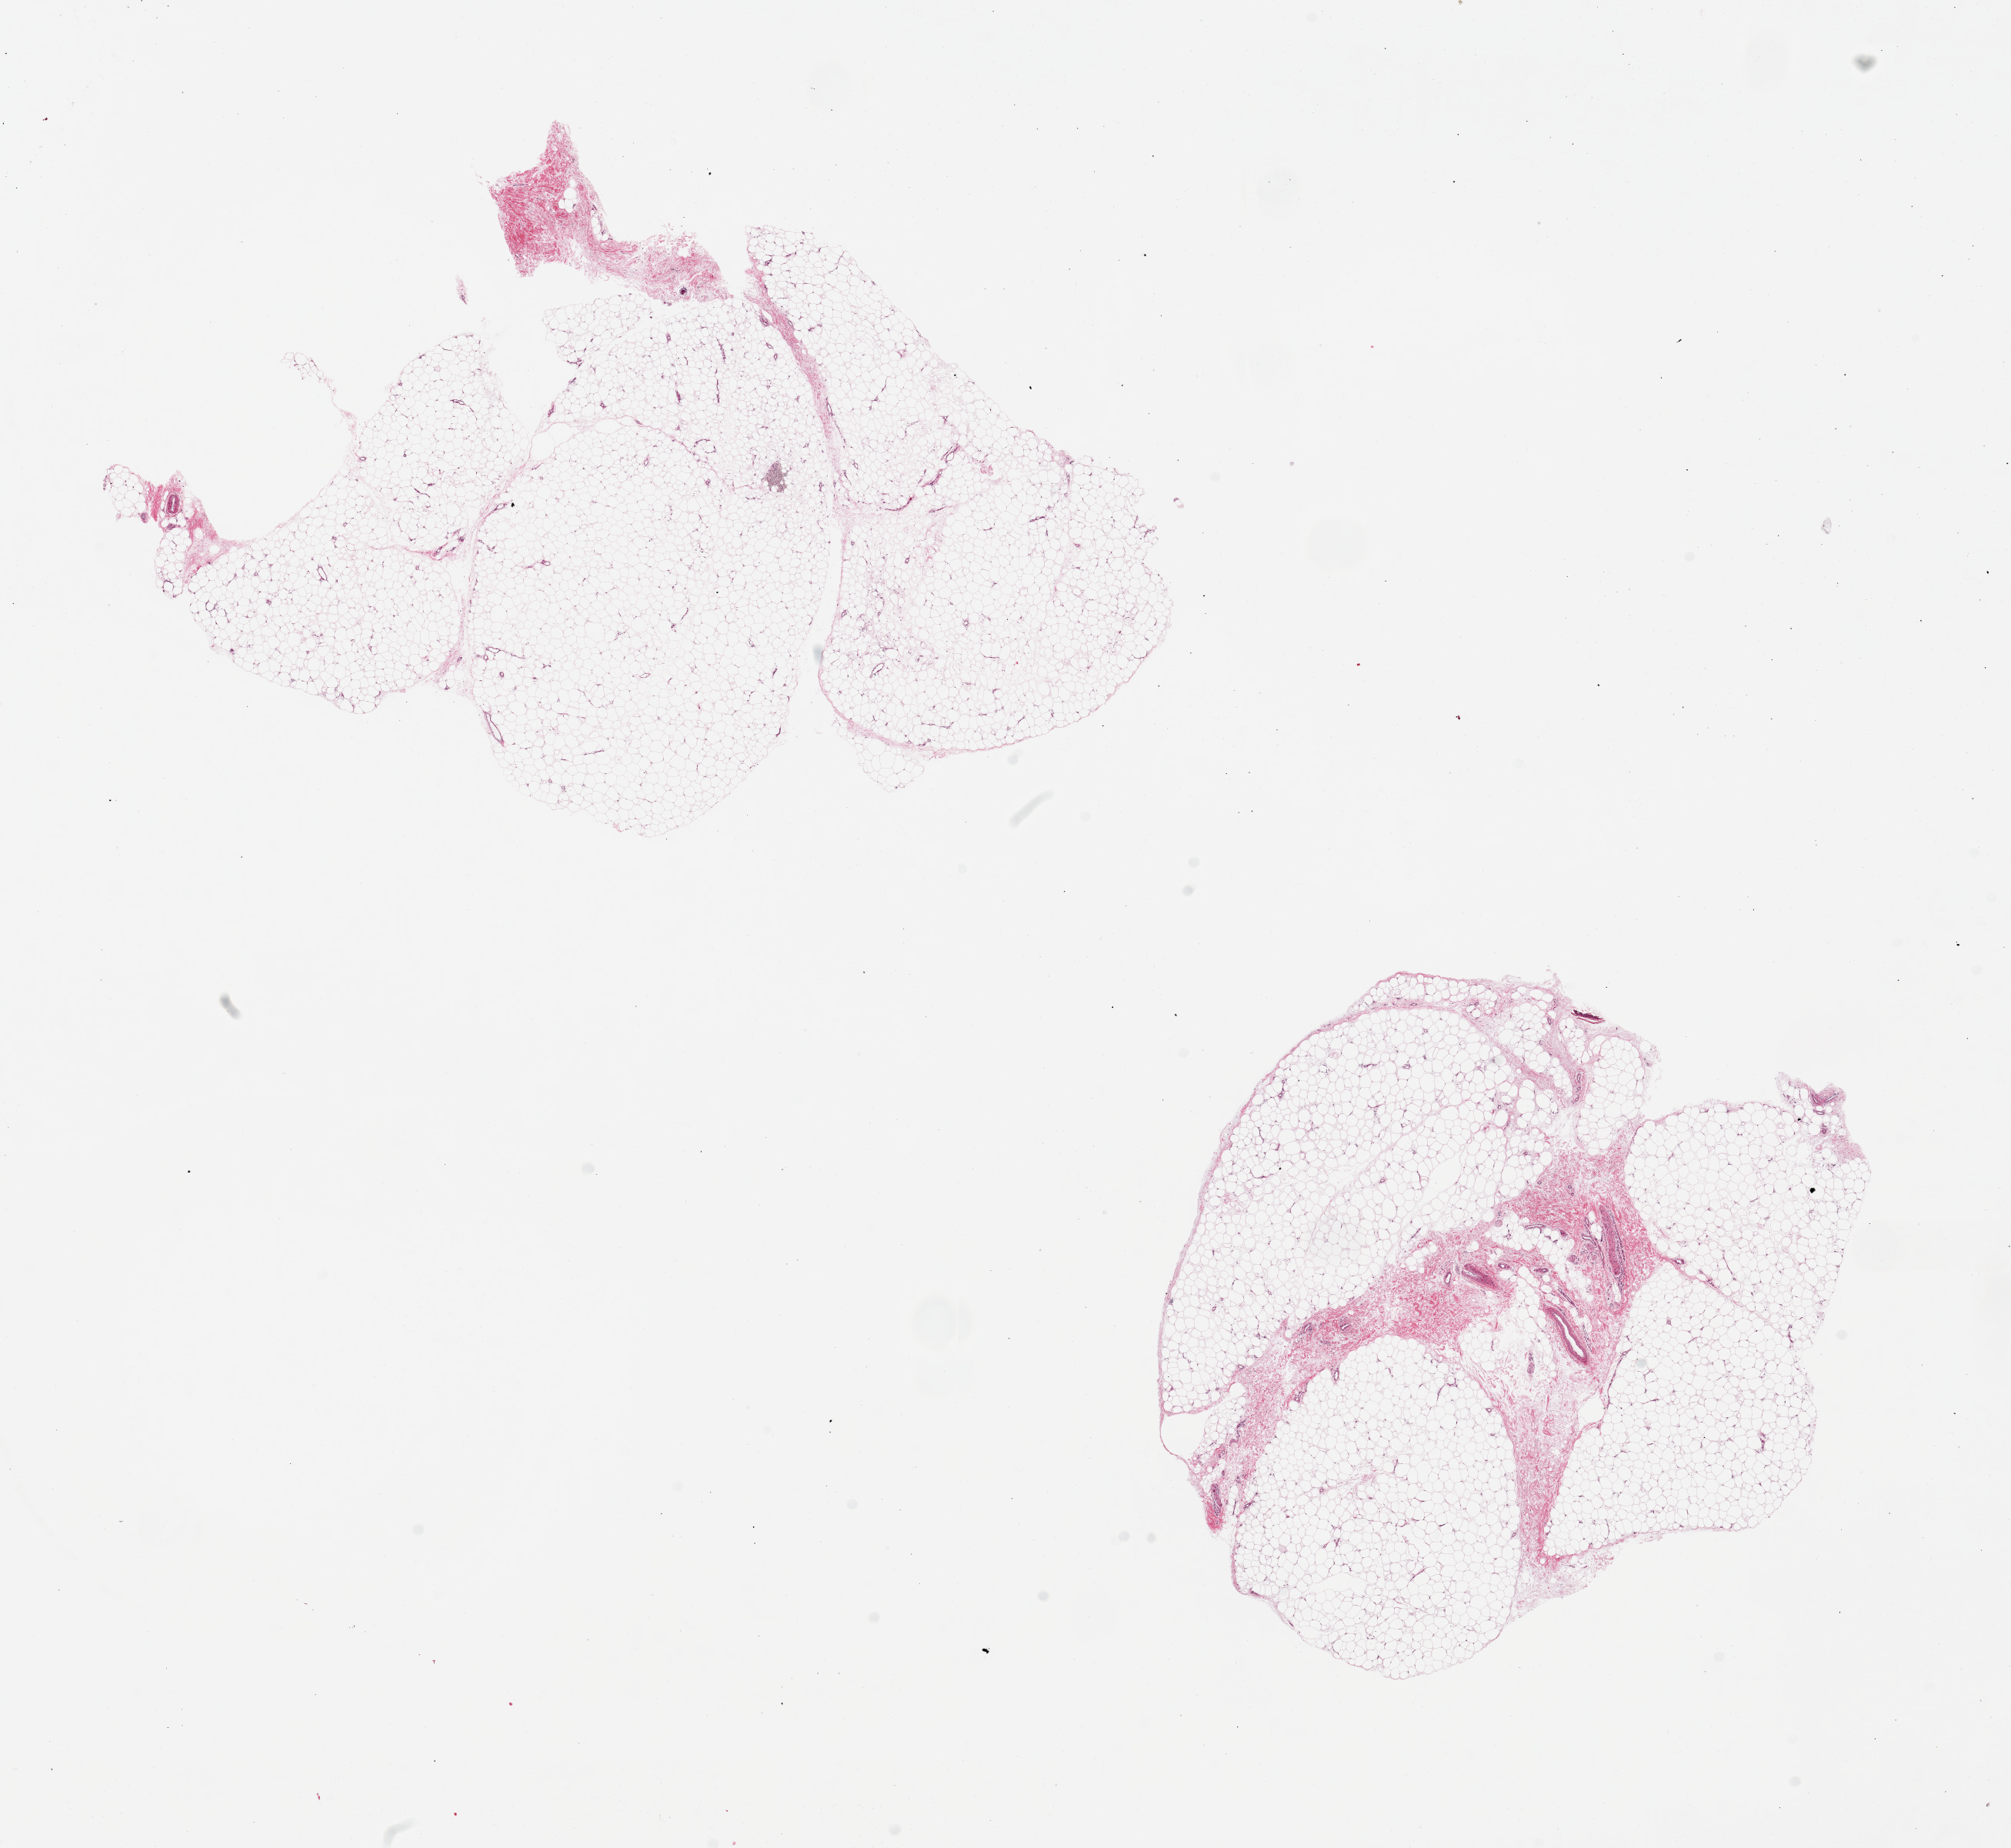
Digitized haematoxylin and eosin-stained section — low-resolution overview of the scanned area, about 20.7 x 19.0 mm; PAXgene-fixed paraffin-embedded (PFPE) section; section of adipose tissue (target tissue); tissue donor sample. Female donor.
- review note (as recorded): 2 pieces, 10x7 & 7x6mm; no fixation artifacts